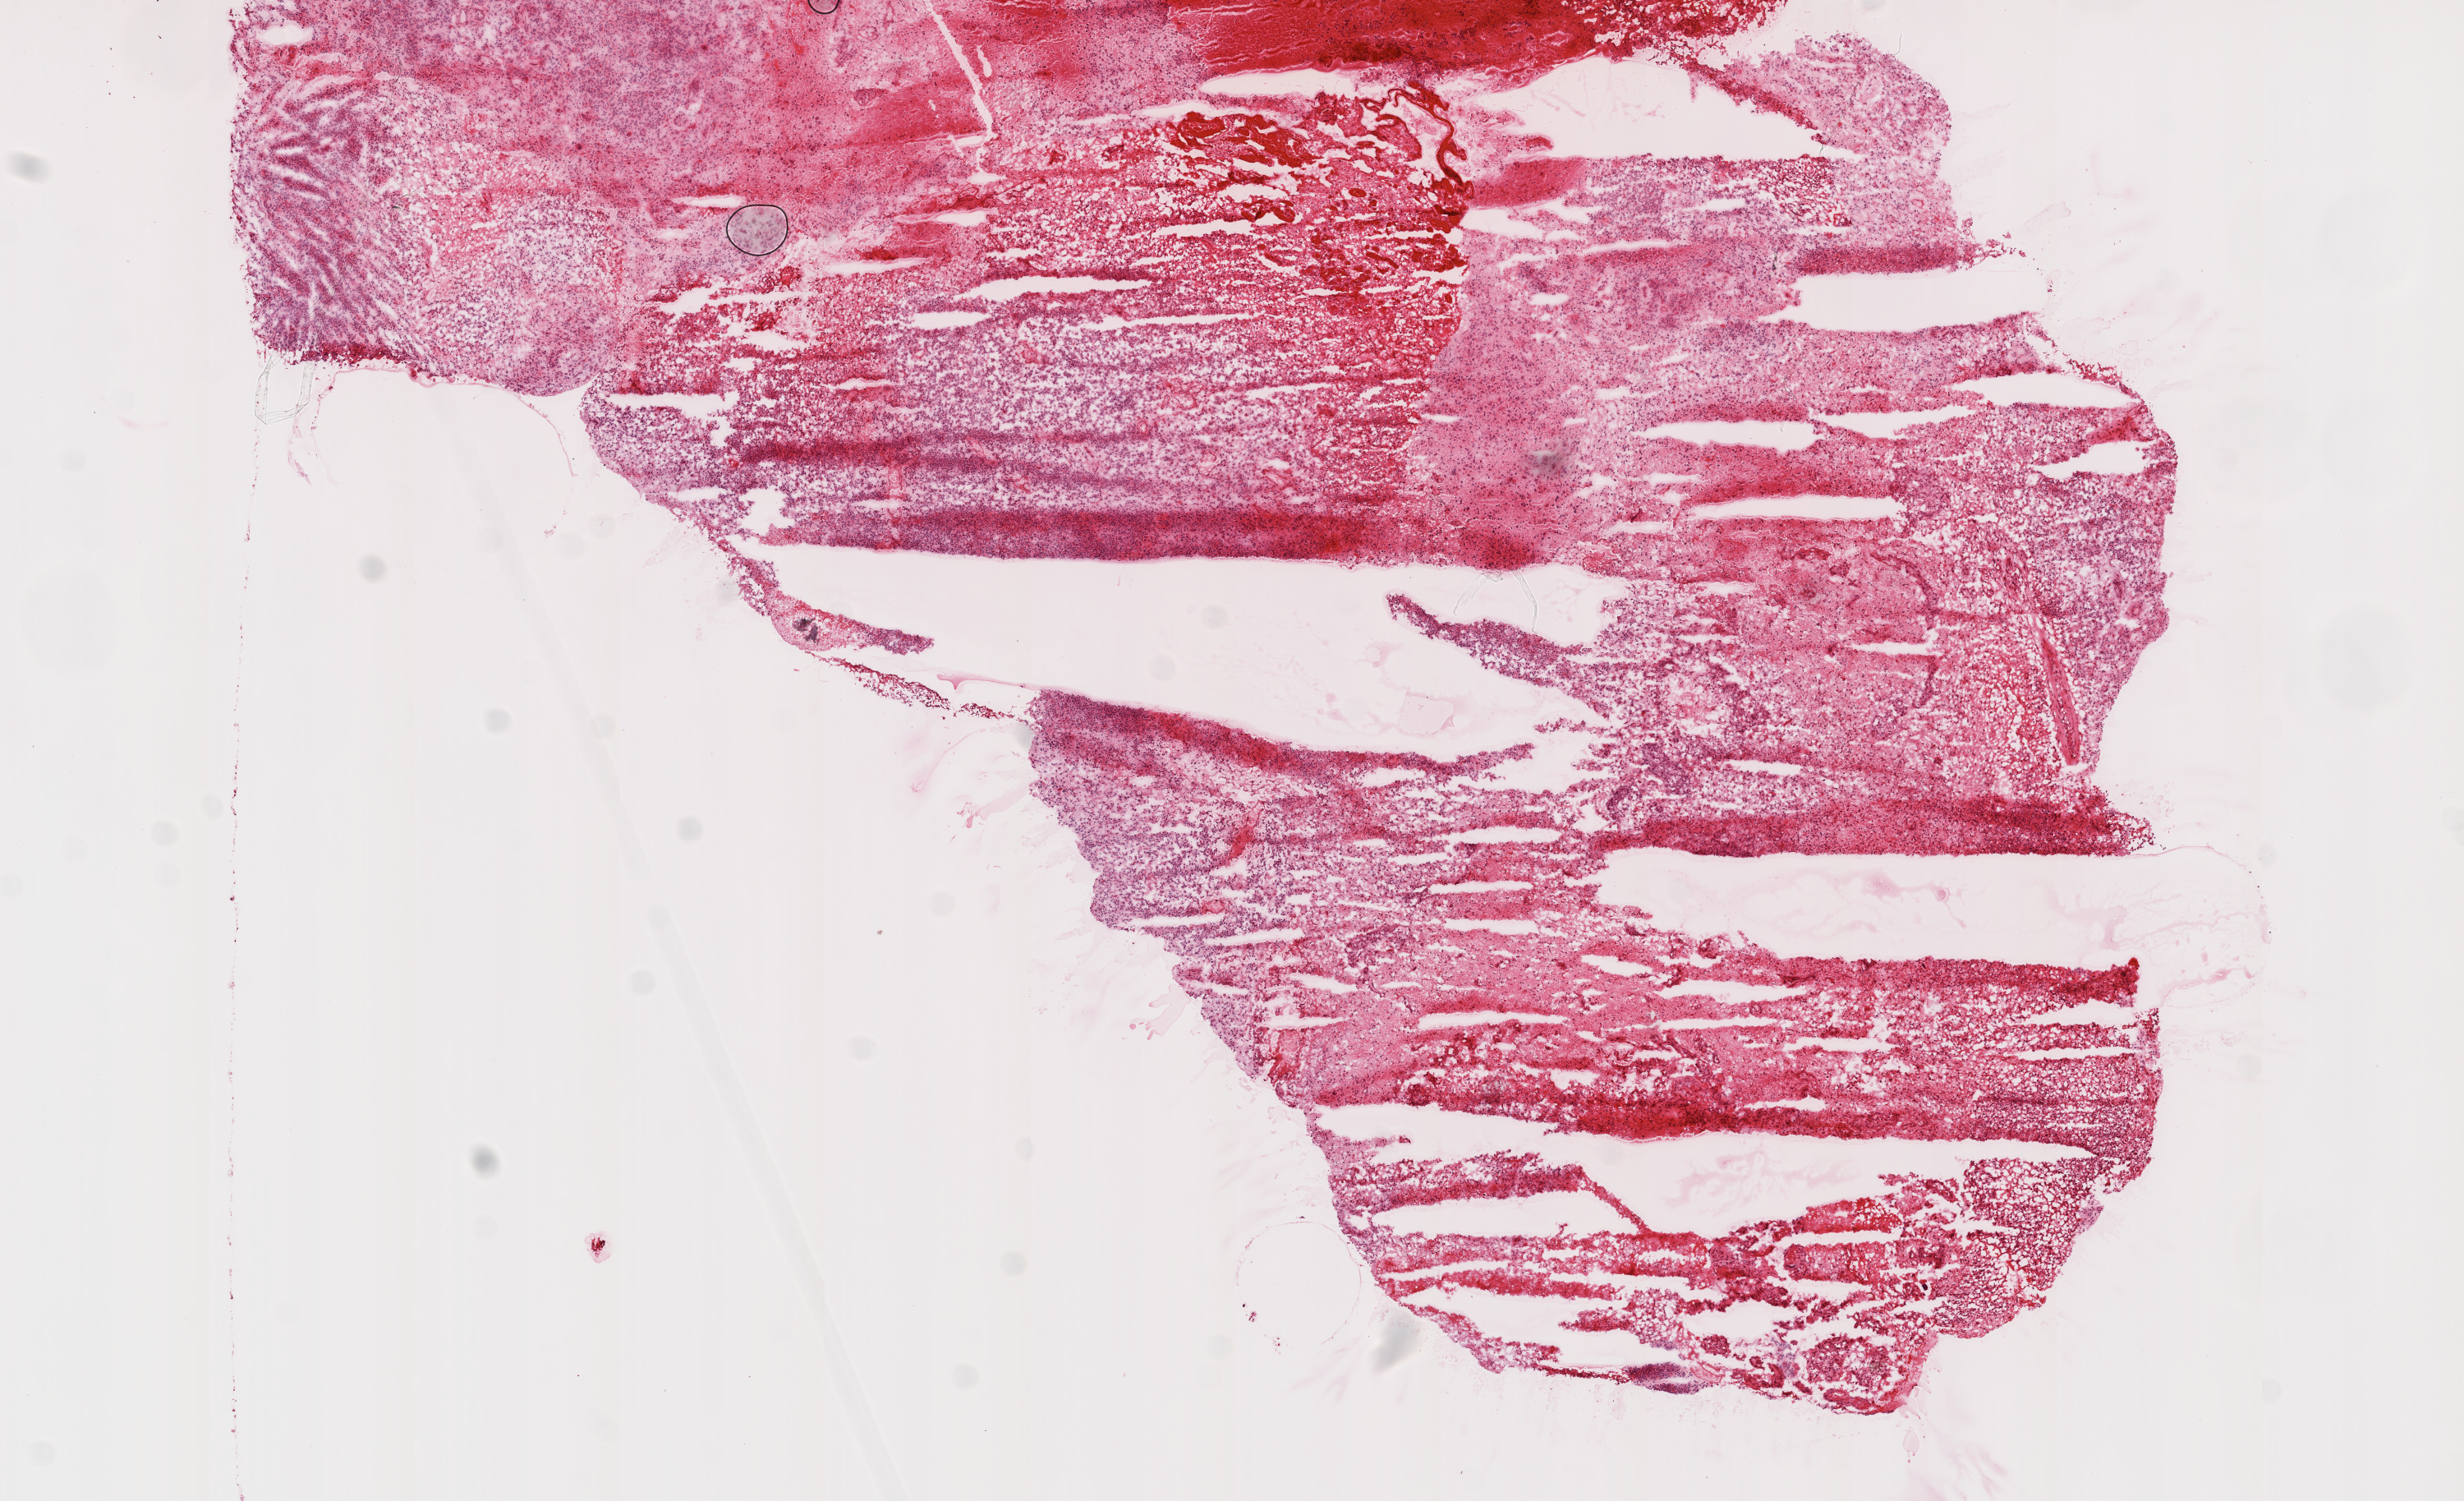
Hematoxylin and eosin (H&E) stained whole-slide image — a low-resolution overview of the entire scanned area, about 12.0 x 7.3 mm. Frozen section from the top of the tissue portion. Primary tumour sample from the brain. Female, age 47 years at initial diagnosis. Composition of this section per pathologist review: tumour cells 70%, tumour nuclei 80%, normal cells 0%, stromal cells 0%, necrosis 30%.
Pathologic diagnosis: Glioblastoma.